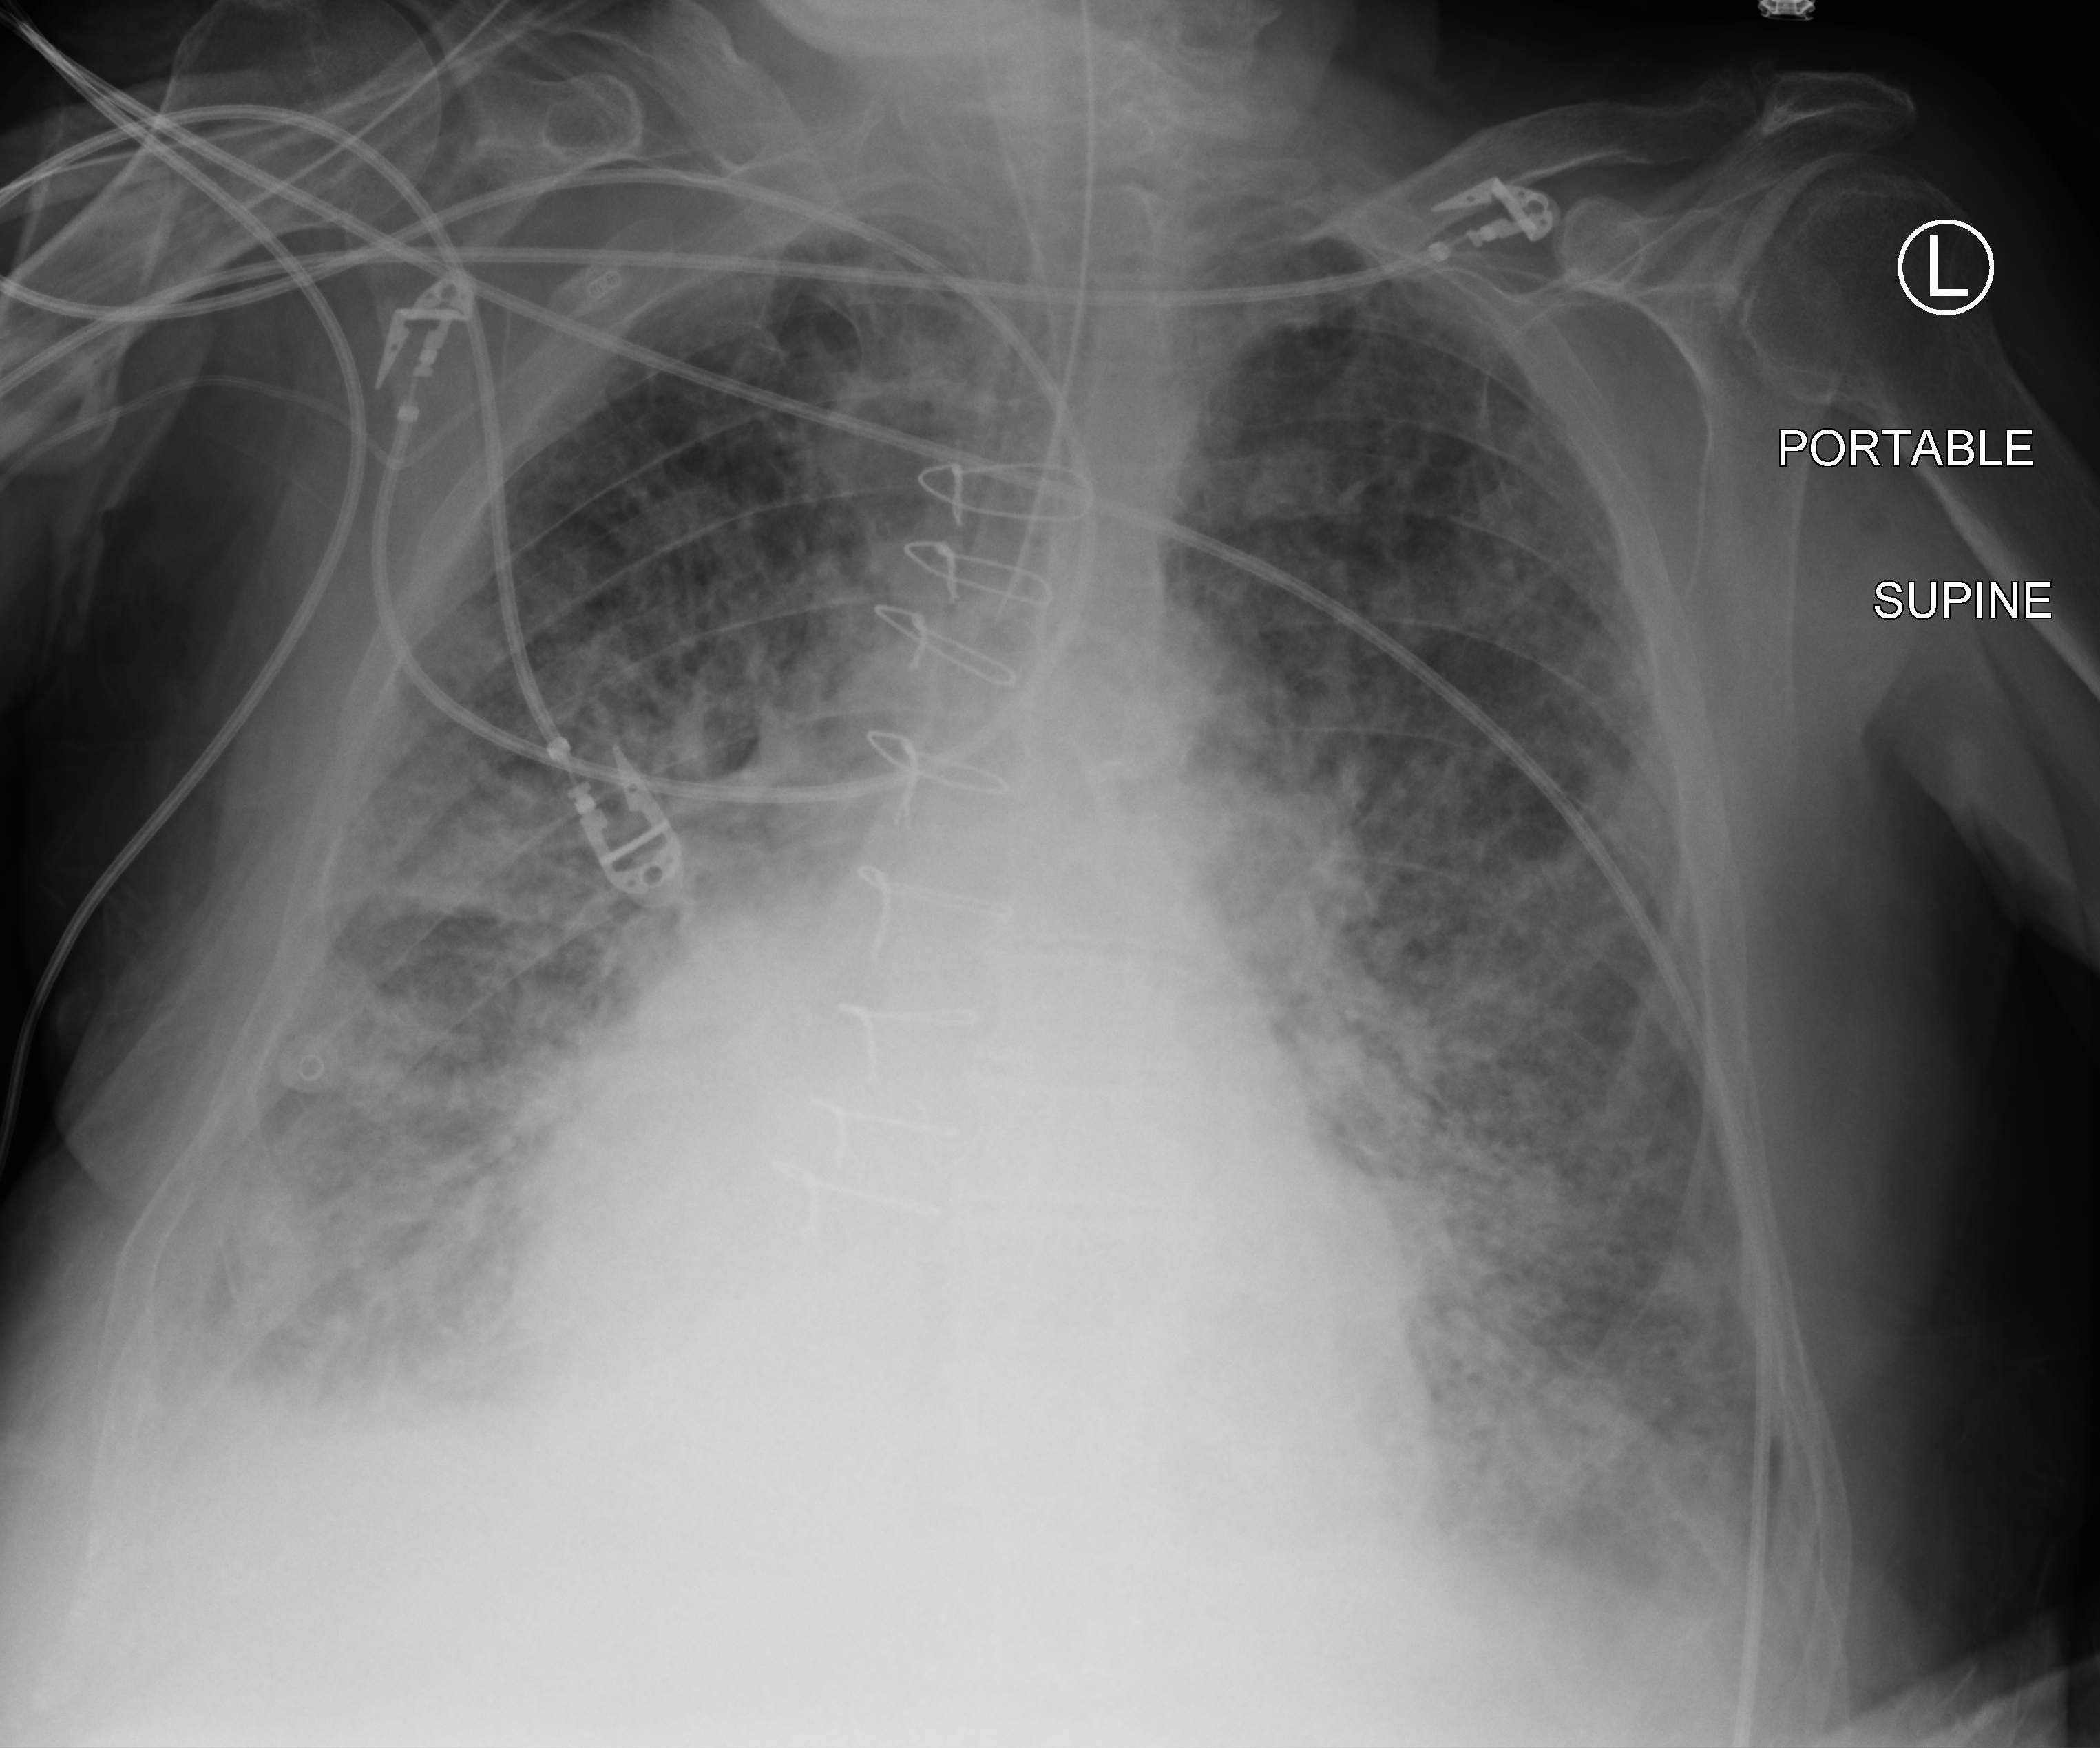
Bedside chest radiograph (computed radiography). Male patient hospitalised with COVID-19, age 75–90 years.
Hospital-stay facts (about this admission, not read from this image; timing relative to this image not recorded): mechanically ventilated during this hospital stay: yes.